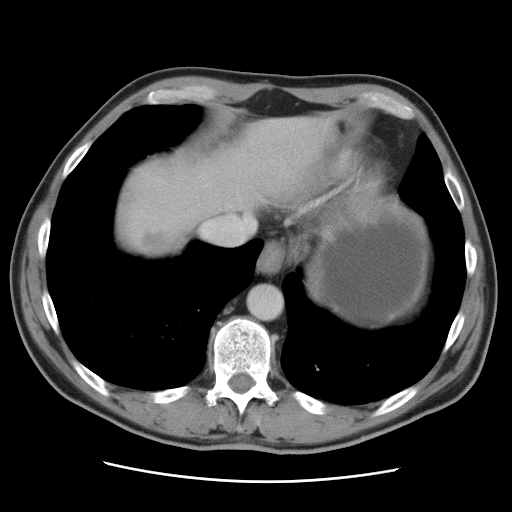
Contrast-enhanced abdominal CT, one axial slice. Position 80 of 89 along the scan axis. 120 kVp. Intravenous contrast given. Soft-tissue window (W 400 / L 40 HU). 512 × 512 image matrix, field of view 366 × 366 mm. Male patient, age 59 years. From the clinical record (not read from this slice): diagnosis: colorectal cancer liver metastases, imaged before liver resection; multiple liver metastases: yes; largest metastasis: 0.6 cm.
Annotated regions visible in this slice (manually delineated by an expert):
- hepatic veins: bounding box (x1, y1, x2, y2) in pixels: (202, 206, 254, 243)
- liver: (114, 115, 328, 258)
- planned liver remnant (the part of the liver to remain after resection): (143, 116, 328, 223)
- liver metastasis: (135, 229, 193, 256)